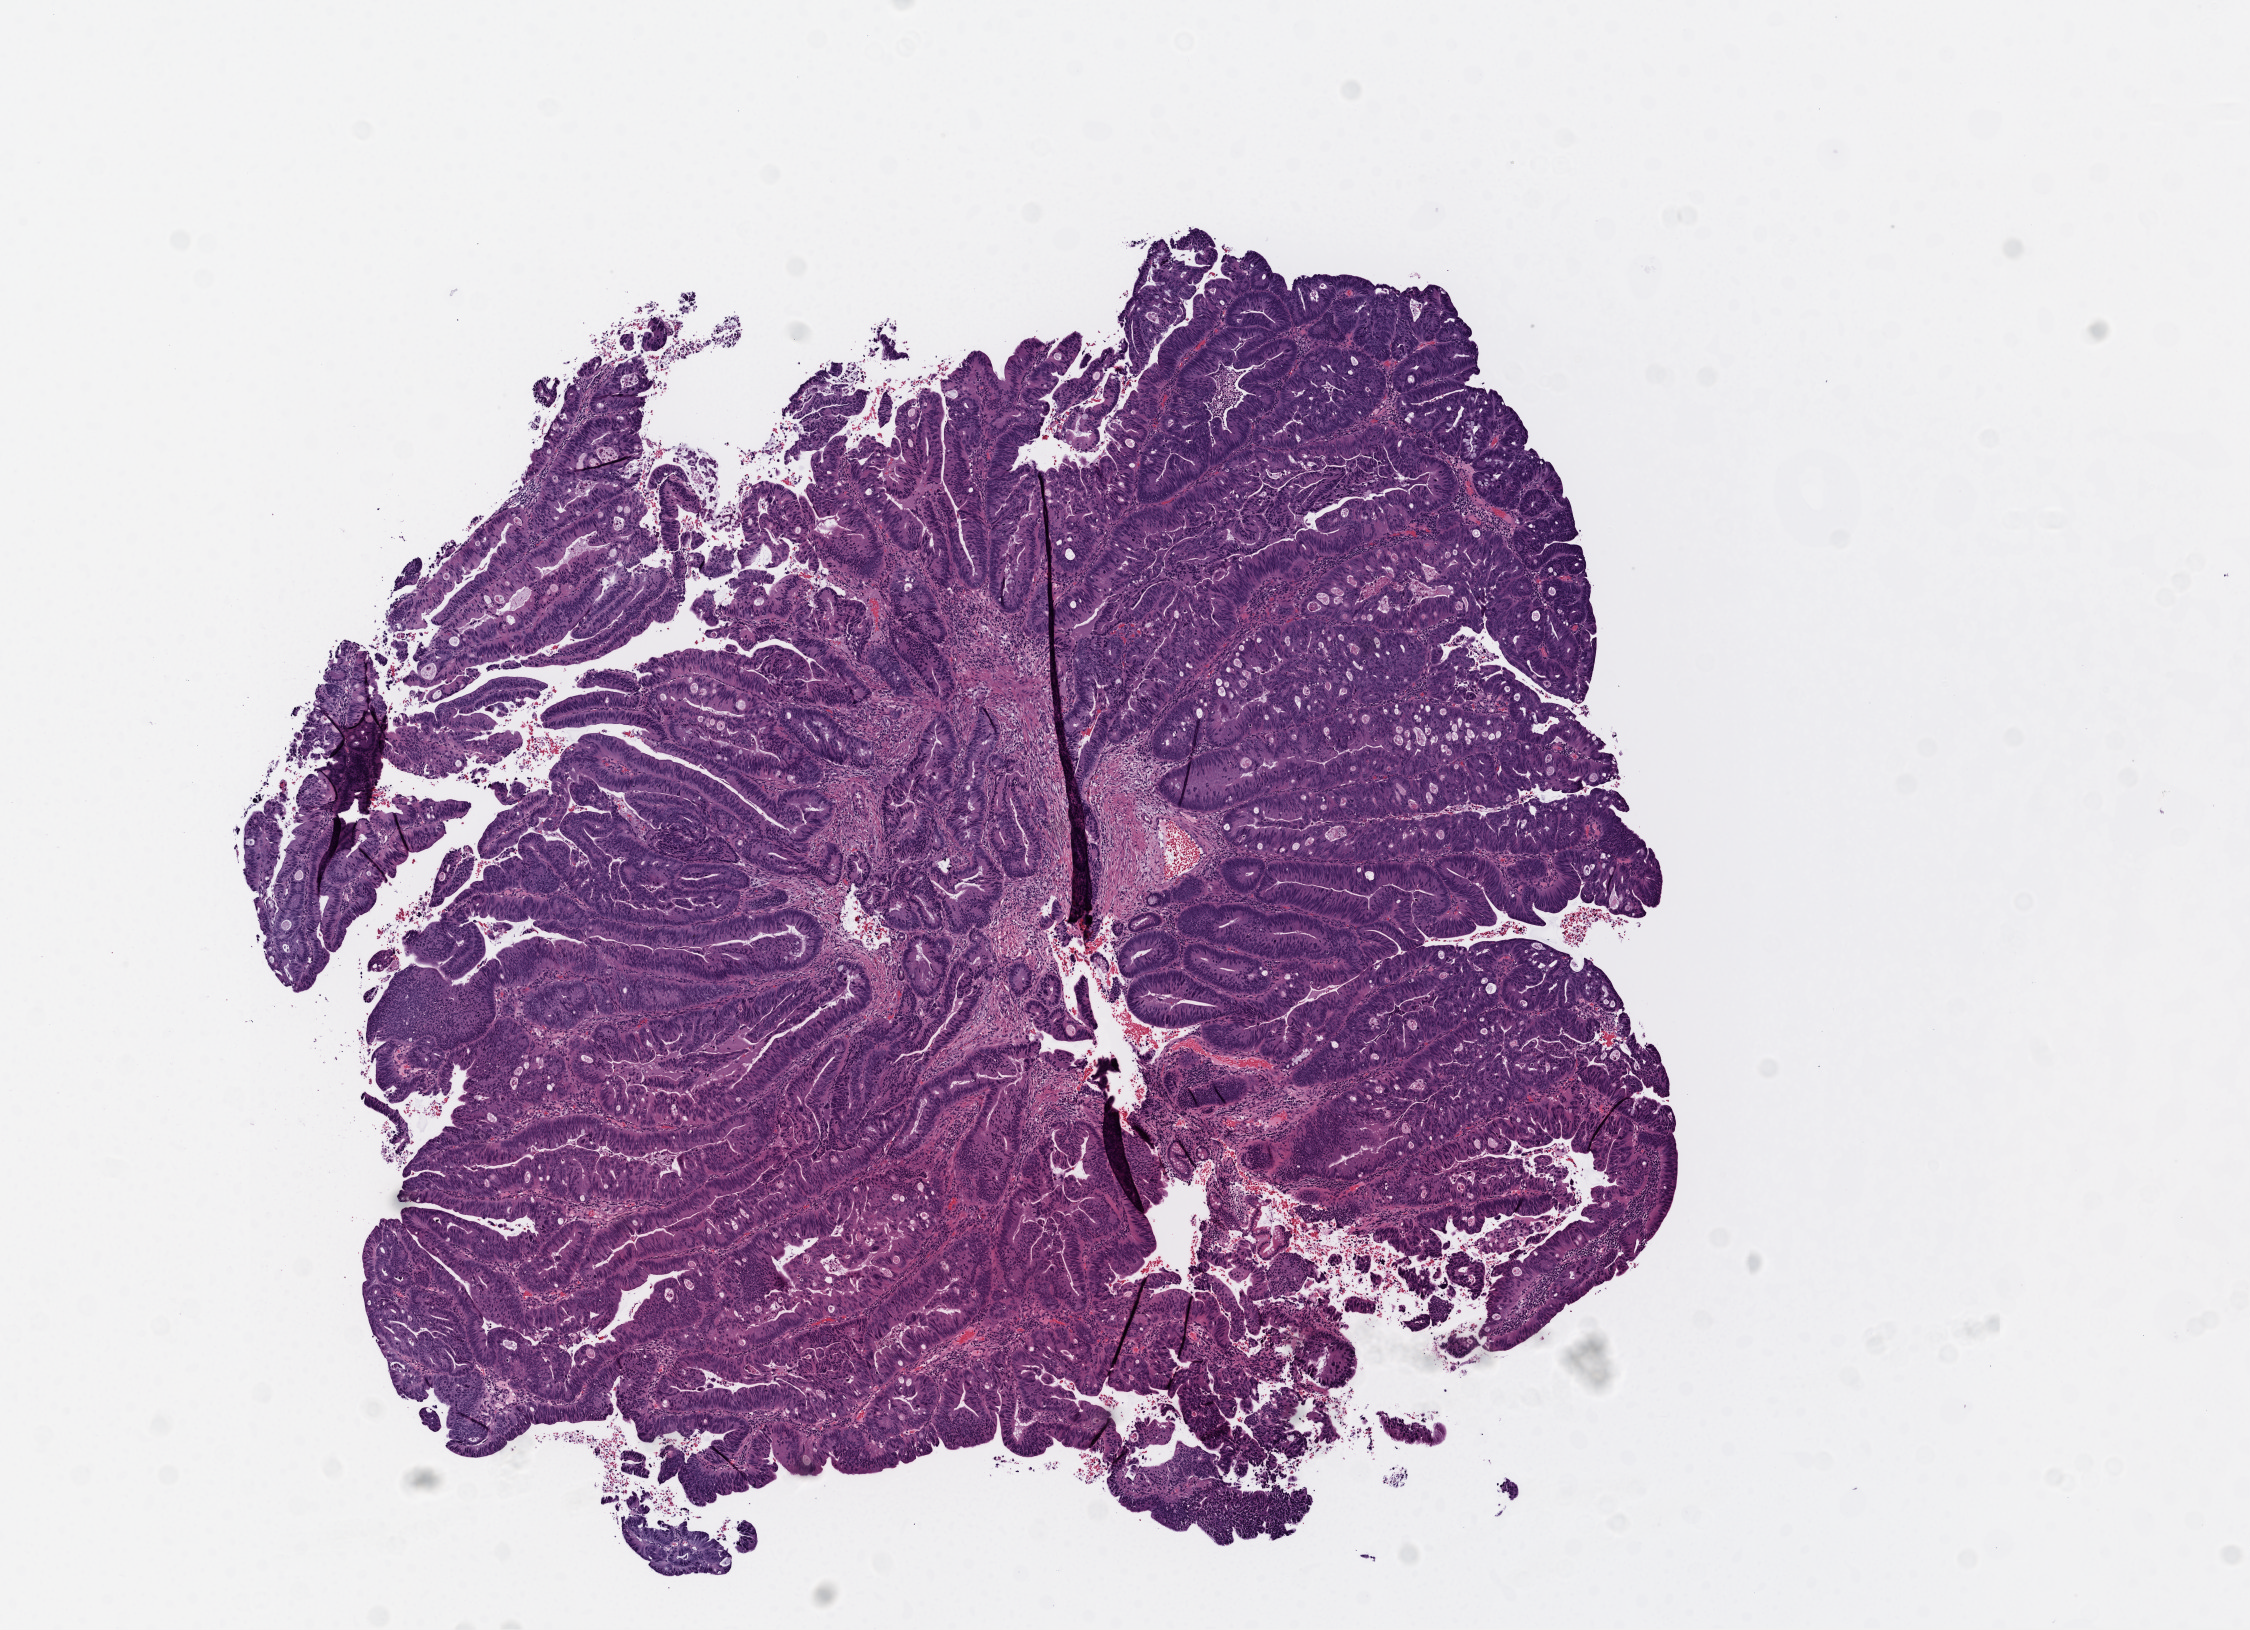
Whole-slide histology image, H&E-stained — whole scanned area (about 9.0 x 6.5 mm, from a 20x scan) shown as a low-resolution overview; frozen section; primary tumour sample from the colon. Female patient; age at initial diagnosis 57 years. Composition of this section per pathologist review: tumour cells 87%, tumour nuclei 90%, normal cells 0%, stromal cells 10%, necrosis 3%.
* TNM: T4 N0 M1
* histologic diagnosis: Adenocarcinoma, NOS
* AJCC pathologic stage: IV (6th edition)